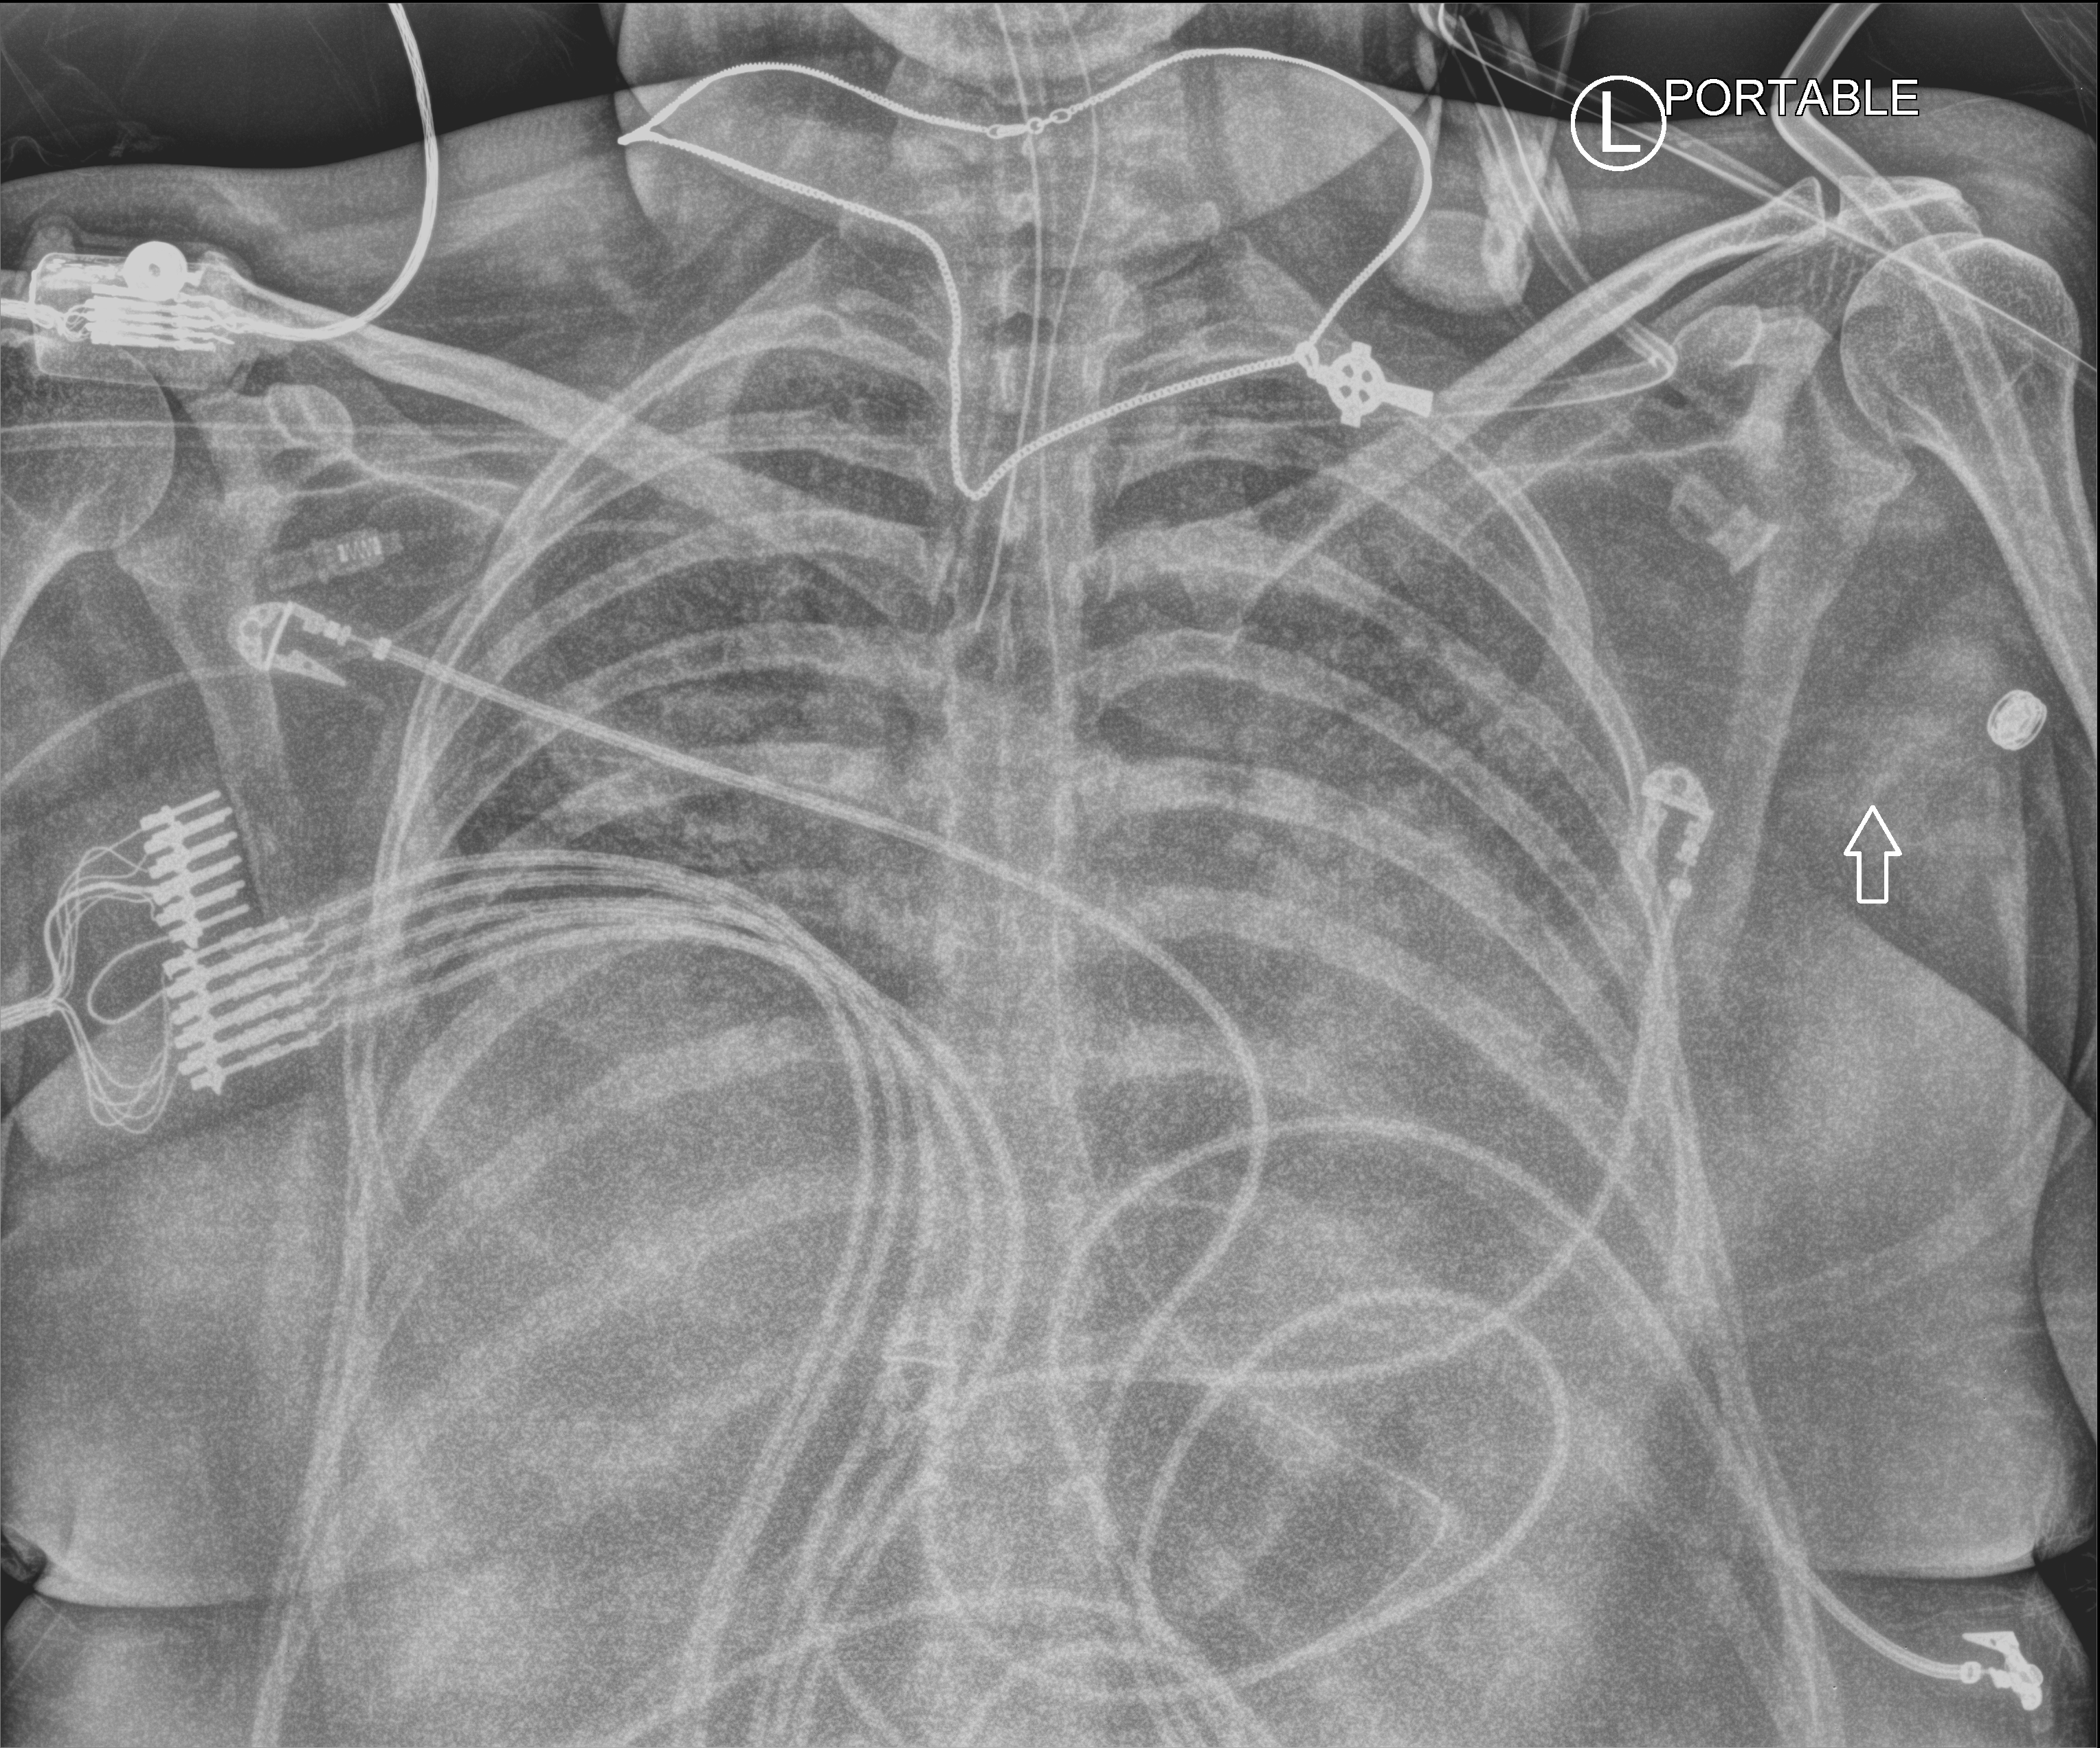
Bedside chest radiograph (computed radiography), anteroposterior (AP) projection. Female patient hospitalised with COVID-19, age 18–59 years.
Admission-level facts for this patient (not findings on this image; timing relative to this image not recorded): length of hospital stay: 73 days; other chronic lung disease (admission record): yes.